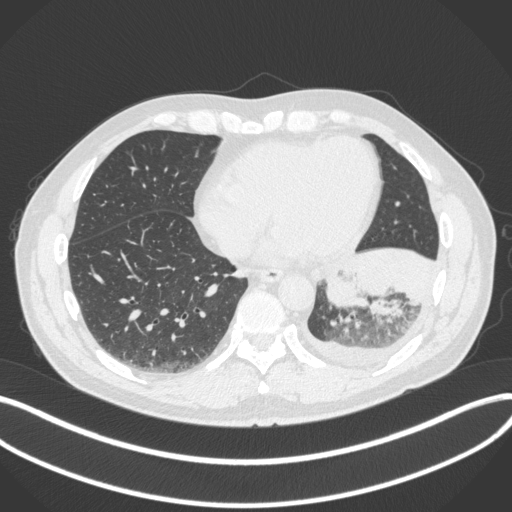
Chest CT, one axial slice; slice 114 of 350 in the series (ordered by position); reconstruction kernel B31f; lung window (W 1500 / L -600 HU); 512 × 512 image matrix, field of view 400 × 400 mm. Patient: male, 58 years. Case-level facts recorded for this patient, not image findings: clinical TNM (as recorded): T3 N1 M1b.
Structures marked on this image (bounding box drawn by a radiologist):
- lung tumour (recorded histology: small cell carcinoma): bounding box (x1, y1, x2, y2) in pixels: (323, 264, 369, 311)